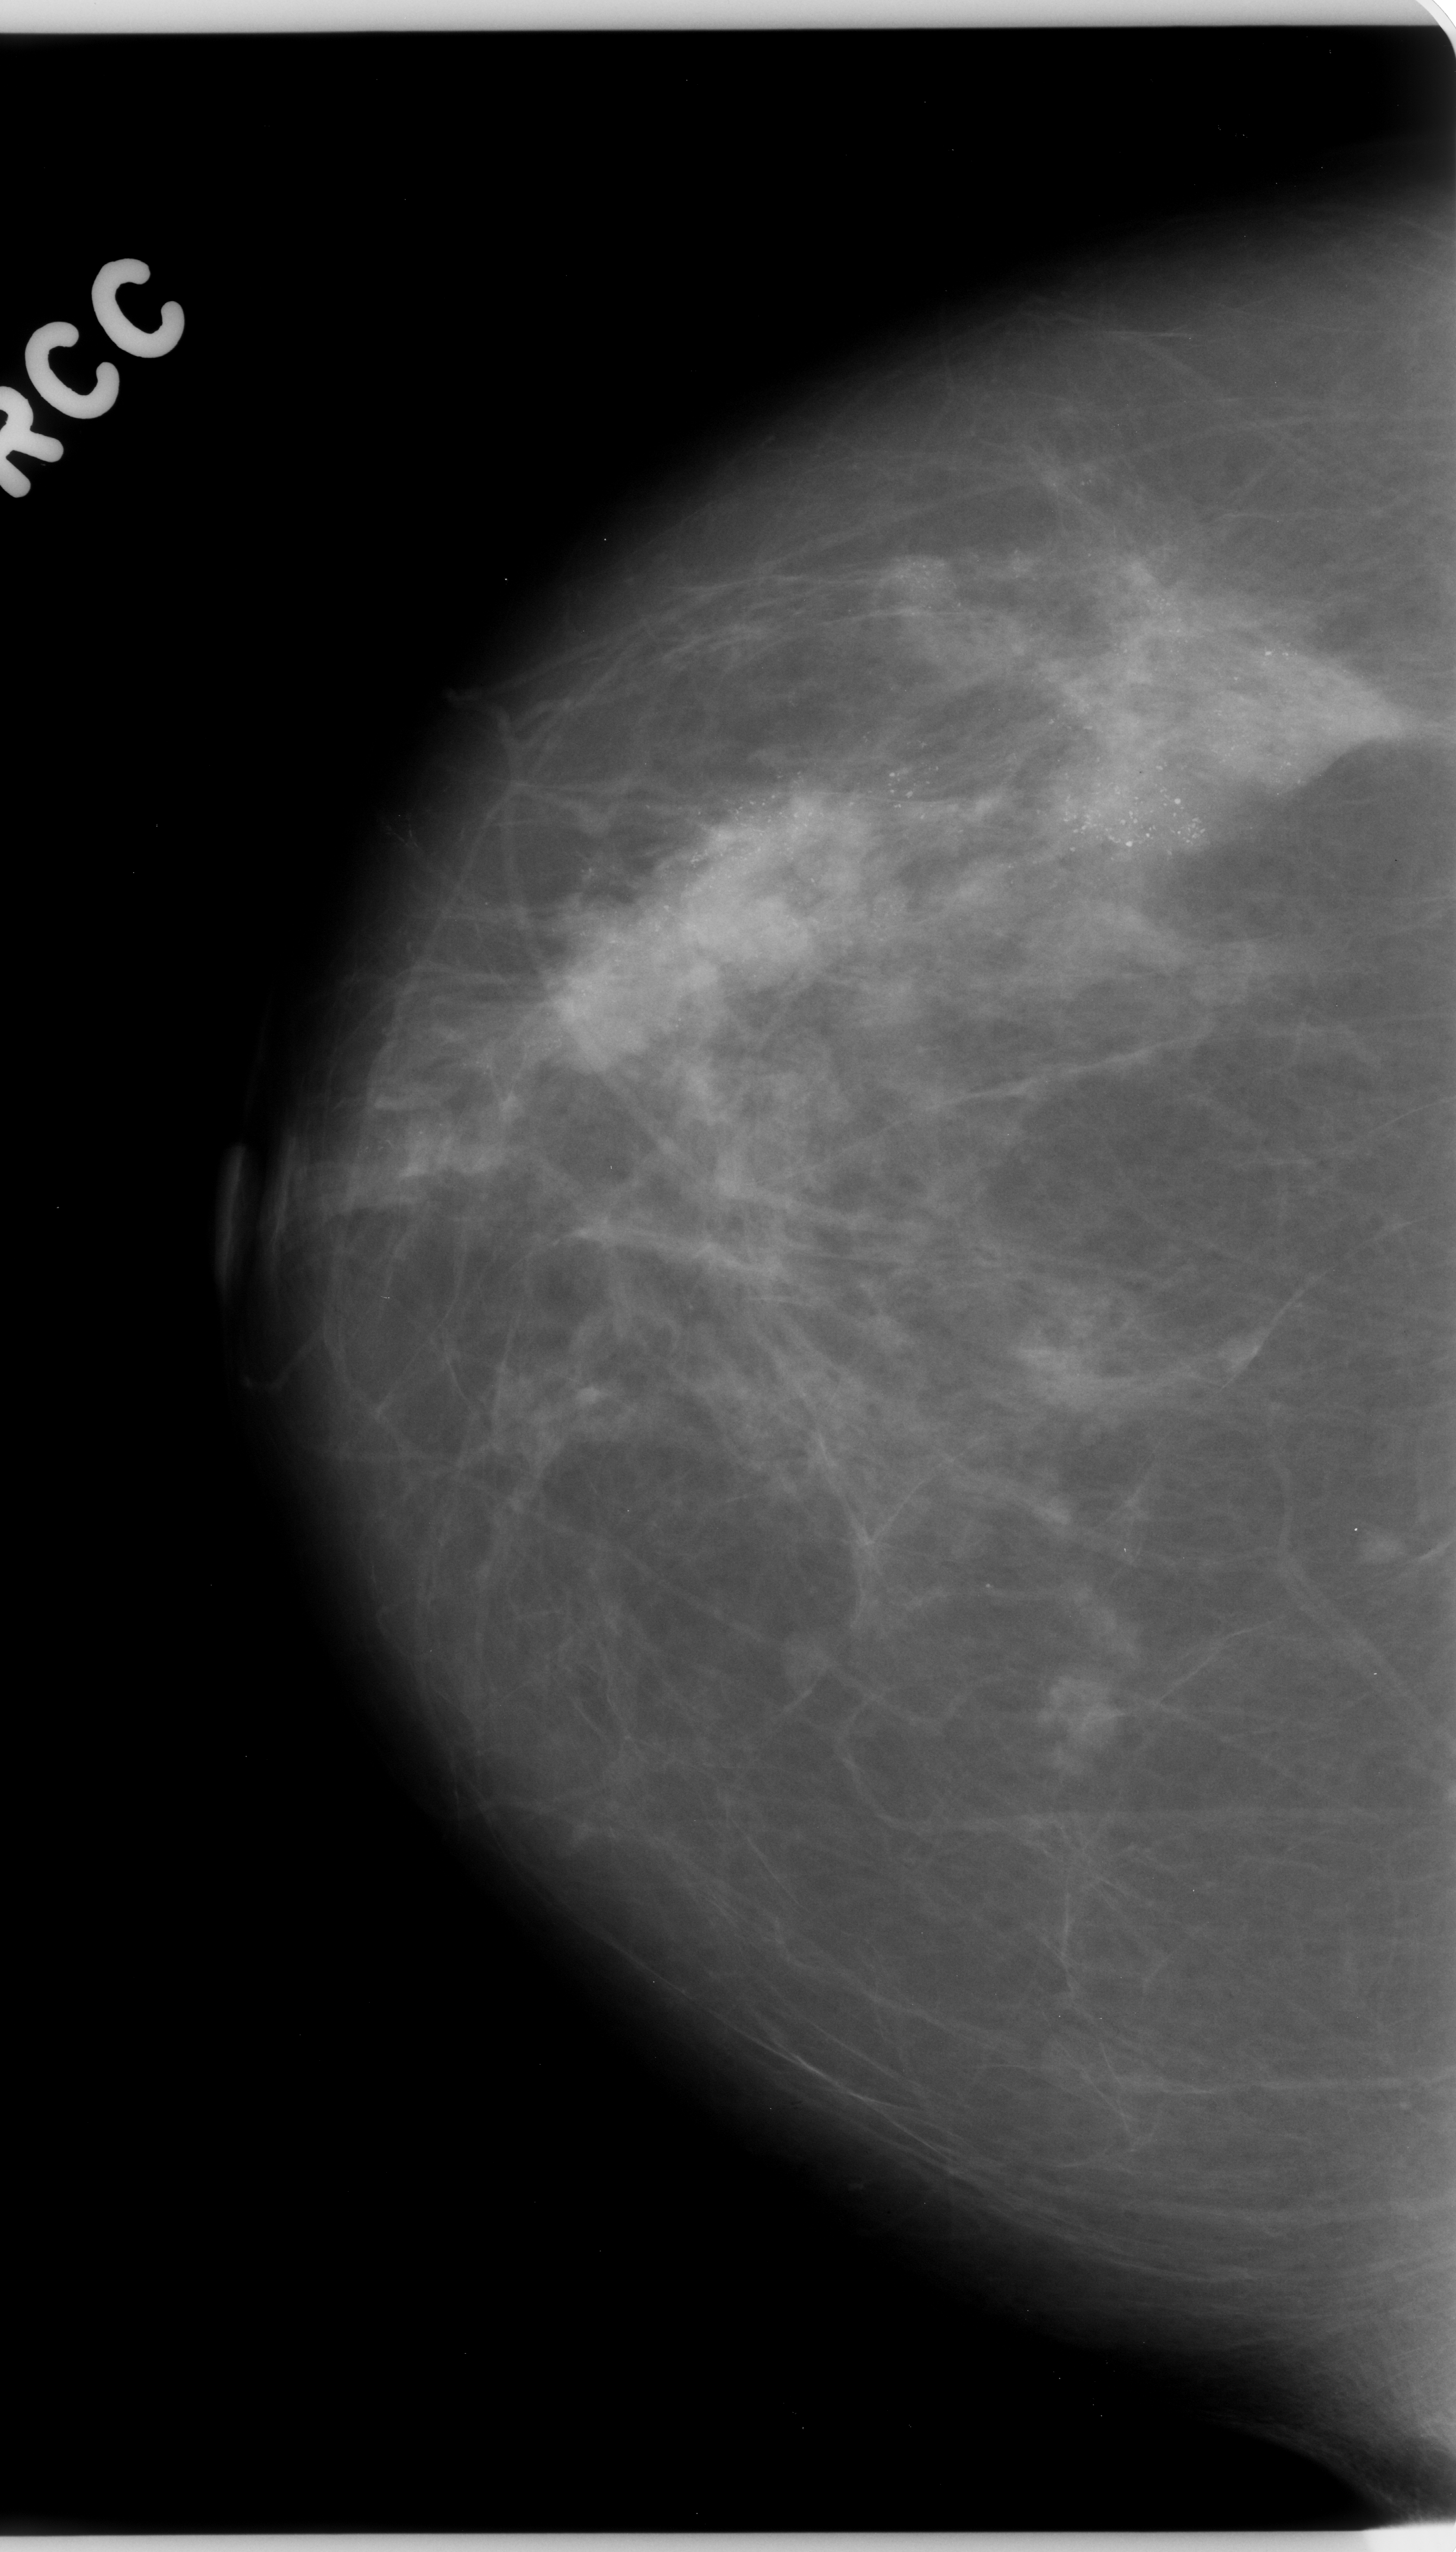
Scanned film-screen mammogram, right breast, craniocaudal (CC) view, breast composition: scattered fibroglandular densities (BI-RADS density category 2 of 4).
Abnormality record for this image: calcifications, morphology pleomorphic, distribution regional; BI-RADS assessment category 5; pathology (as recorded): malignant.